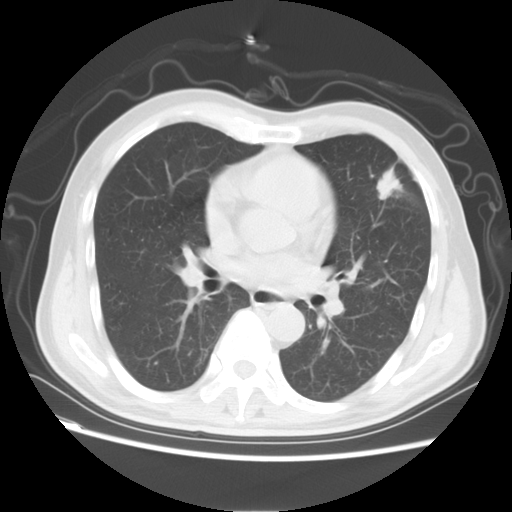
Chest CT, one axial slice; slice 33 of 64 in the series (ordered by position); 120 kVp; lung window (W 1500 / L -600 HU); 512 × 512 image matrix, field of view 368 × 368 mm. Male patient, age 60 years. From the clinical record (not read from this slice): clinical TNM (as recorded): T2a N0 M0.
Outlined on this slice (rectangle marked by the reading radiologist):
- lung tumour (recorded histology: adenocarcinoma): bounding box (x1, y1, x2, y2) in pixels: (369, 158, 407, 201)